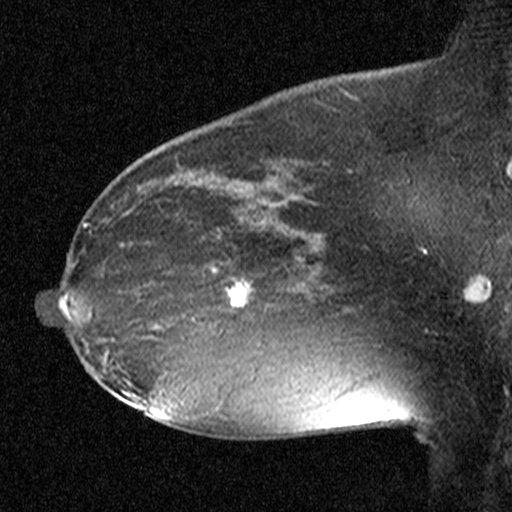
Breast MRI (dynamic contrast-enhanced), one sagittal slice; slice 29 of 44 in the series (ordered by position); dynamic contrast-enhanced study with each time point stored as its own series, time point 2 of 3 at this slice position (early post-contrast, ordered by acquisition time); 1.5 T; TE 4.5 ms, TR 11 ms; 512 × 512 image matrix. Female patient, age 38 years. Case-level facts recorded for this patient, not image findings: setting: breast cancer imaged before/during neoadjuvant chemotherapy; receptor status: HR-positive, HER2-negative.
Annotated regions visible in this slice (semi-automatically segmented with operator editing):
- analysis volume of interest (the breast-tissue region the enhancement analysis was run in; not a lesion): bounding box <182,232,291,349> (left, top, right, bottom; pixels)
- tumour enhancement mask (voxels above the 90 % enhancement threshold inside the analysis volume of interest): <206,232,245,306>